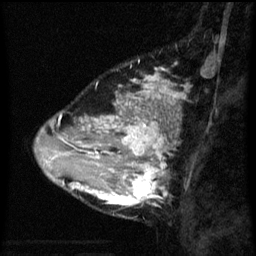
Breast MRI (dynamic contrast-enhanced), one sagittal slice; dynamic contrast-enhanced series, image 2 of 3 at this slice position (ordered by acquisition); 1.5 T; TE 4.2 ms, TR 8 ms; 2.3 mm slice thickness; 256 × 256 image matrix, field of view 180 × 180 mm. Patient: female, 33 years.
Structures marked on this image (semi-automatically segmented with operator editing):
- analysis volume of interest (the breast-tissue region the enhancement analysis was run in; not a lesion): bounding box [x1, y1, x2, y2] px = [71, 118, 171, 207]
- tumour enhancement mask (voxels above the 70 % enhancement threshold inside the analysis volume of interest): [71, 118, 166, 207]